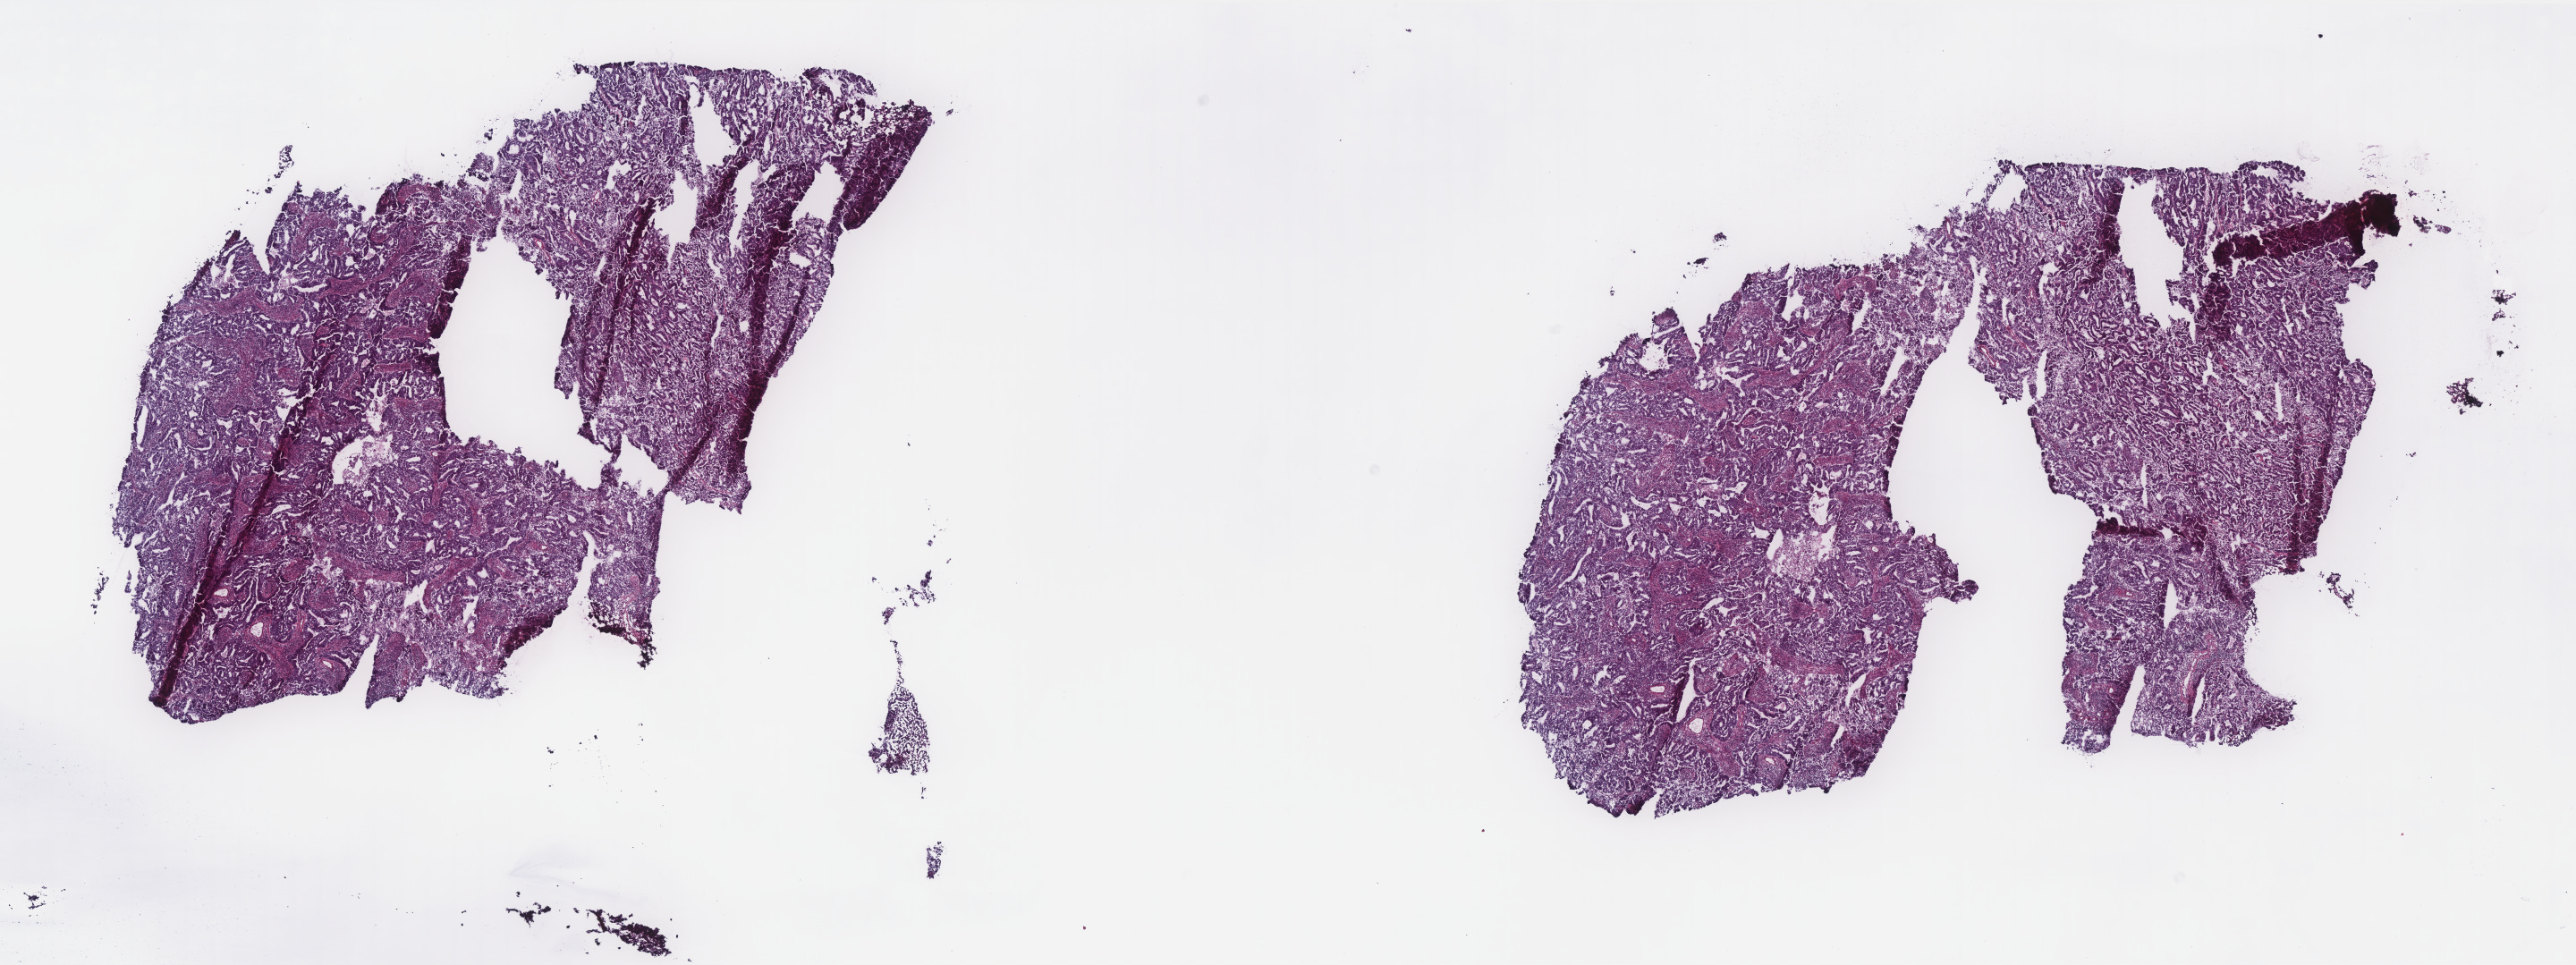
H&E-stained whole-slide image, shown as a low-resolution overview of the whole scanned area (about 23.1 x 8.7 mm); frozen section from the top of the tissue portion; sample: primary tumour, uterus. Patient: female, age at initial diagnosis 74 years. Histologic grade: G2 (moderately differentiated). Composition of this section per pathologist review: tumour cells 100%, tumour nuclei 70%, normal cells 0%, stromal cells 0%, necrosis 0%. Inflammatory infiltration, as recorded: lymphocyte infiltration 0%, monocyte infiltration 0%, neutrophil infiltration 0%.
FIGO stage: IA. Diagnosis: Endometrioid adenocarcinoma, NOS (endometrium).